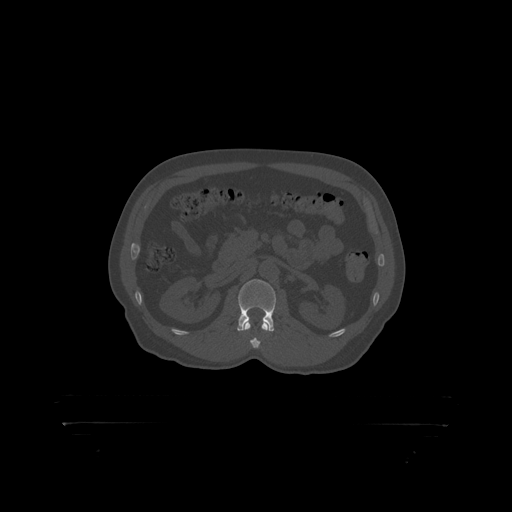
CT including the spine, one axial slice; slice 306 of 399 in the series (ordered by position); 120 kVp; bone window (W 1800 / L 400 HU); 1.25 mm slice thickness; 512 × 512 image matrix. Male patient, age 46 years. From the clinical record (not read from this slice): primary cancer: skin.
Outlined on this slice (semi-automatic segmentation, software-assisted and operator-edited):
- L2 vertebra: bounding box [x1, y1, x2, y2] px = [238, 280, 277, 319]